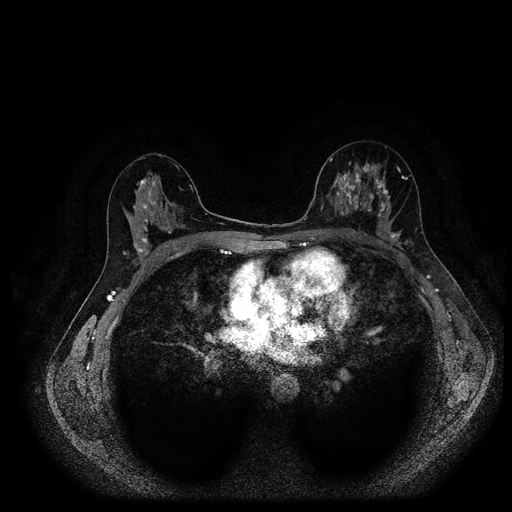
Breast MRI (dynamic contrast-enhanced, multi-phase), one axial slice; slice 57 of 116 in the series (ordered by position); dynamic contrast-enhanced series, time point 2 of 5 at this slice position (early post-contrast); 1.5 T; TE 2.7 ms, TR 5.4 ms; 2 mm slice thickness; 512 × 512 image matrix, field of view 340 × 340 mm. Female patient, age 40 years.
Outlined on this slice (semi-automatic segmentation, software-assisted and operator-edited):
- breast lesion (labelled 'tumour' in the annotation; benign lesions carry a separate 'benign' label): bounding box <337,171,368,215> (left, top, right, bottom; pixels)